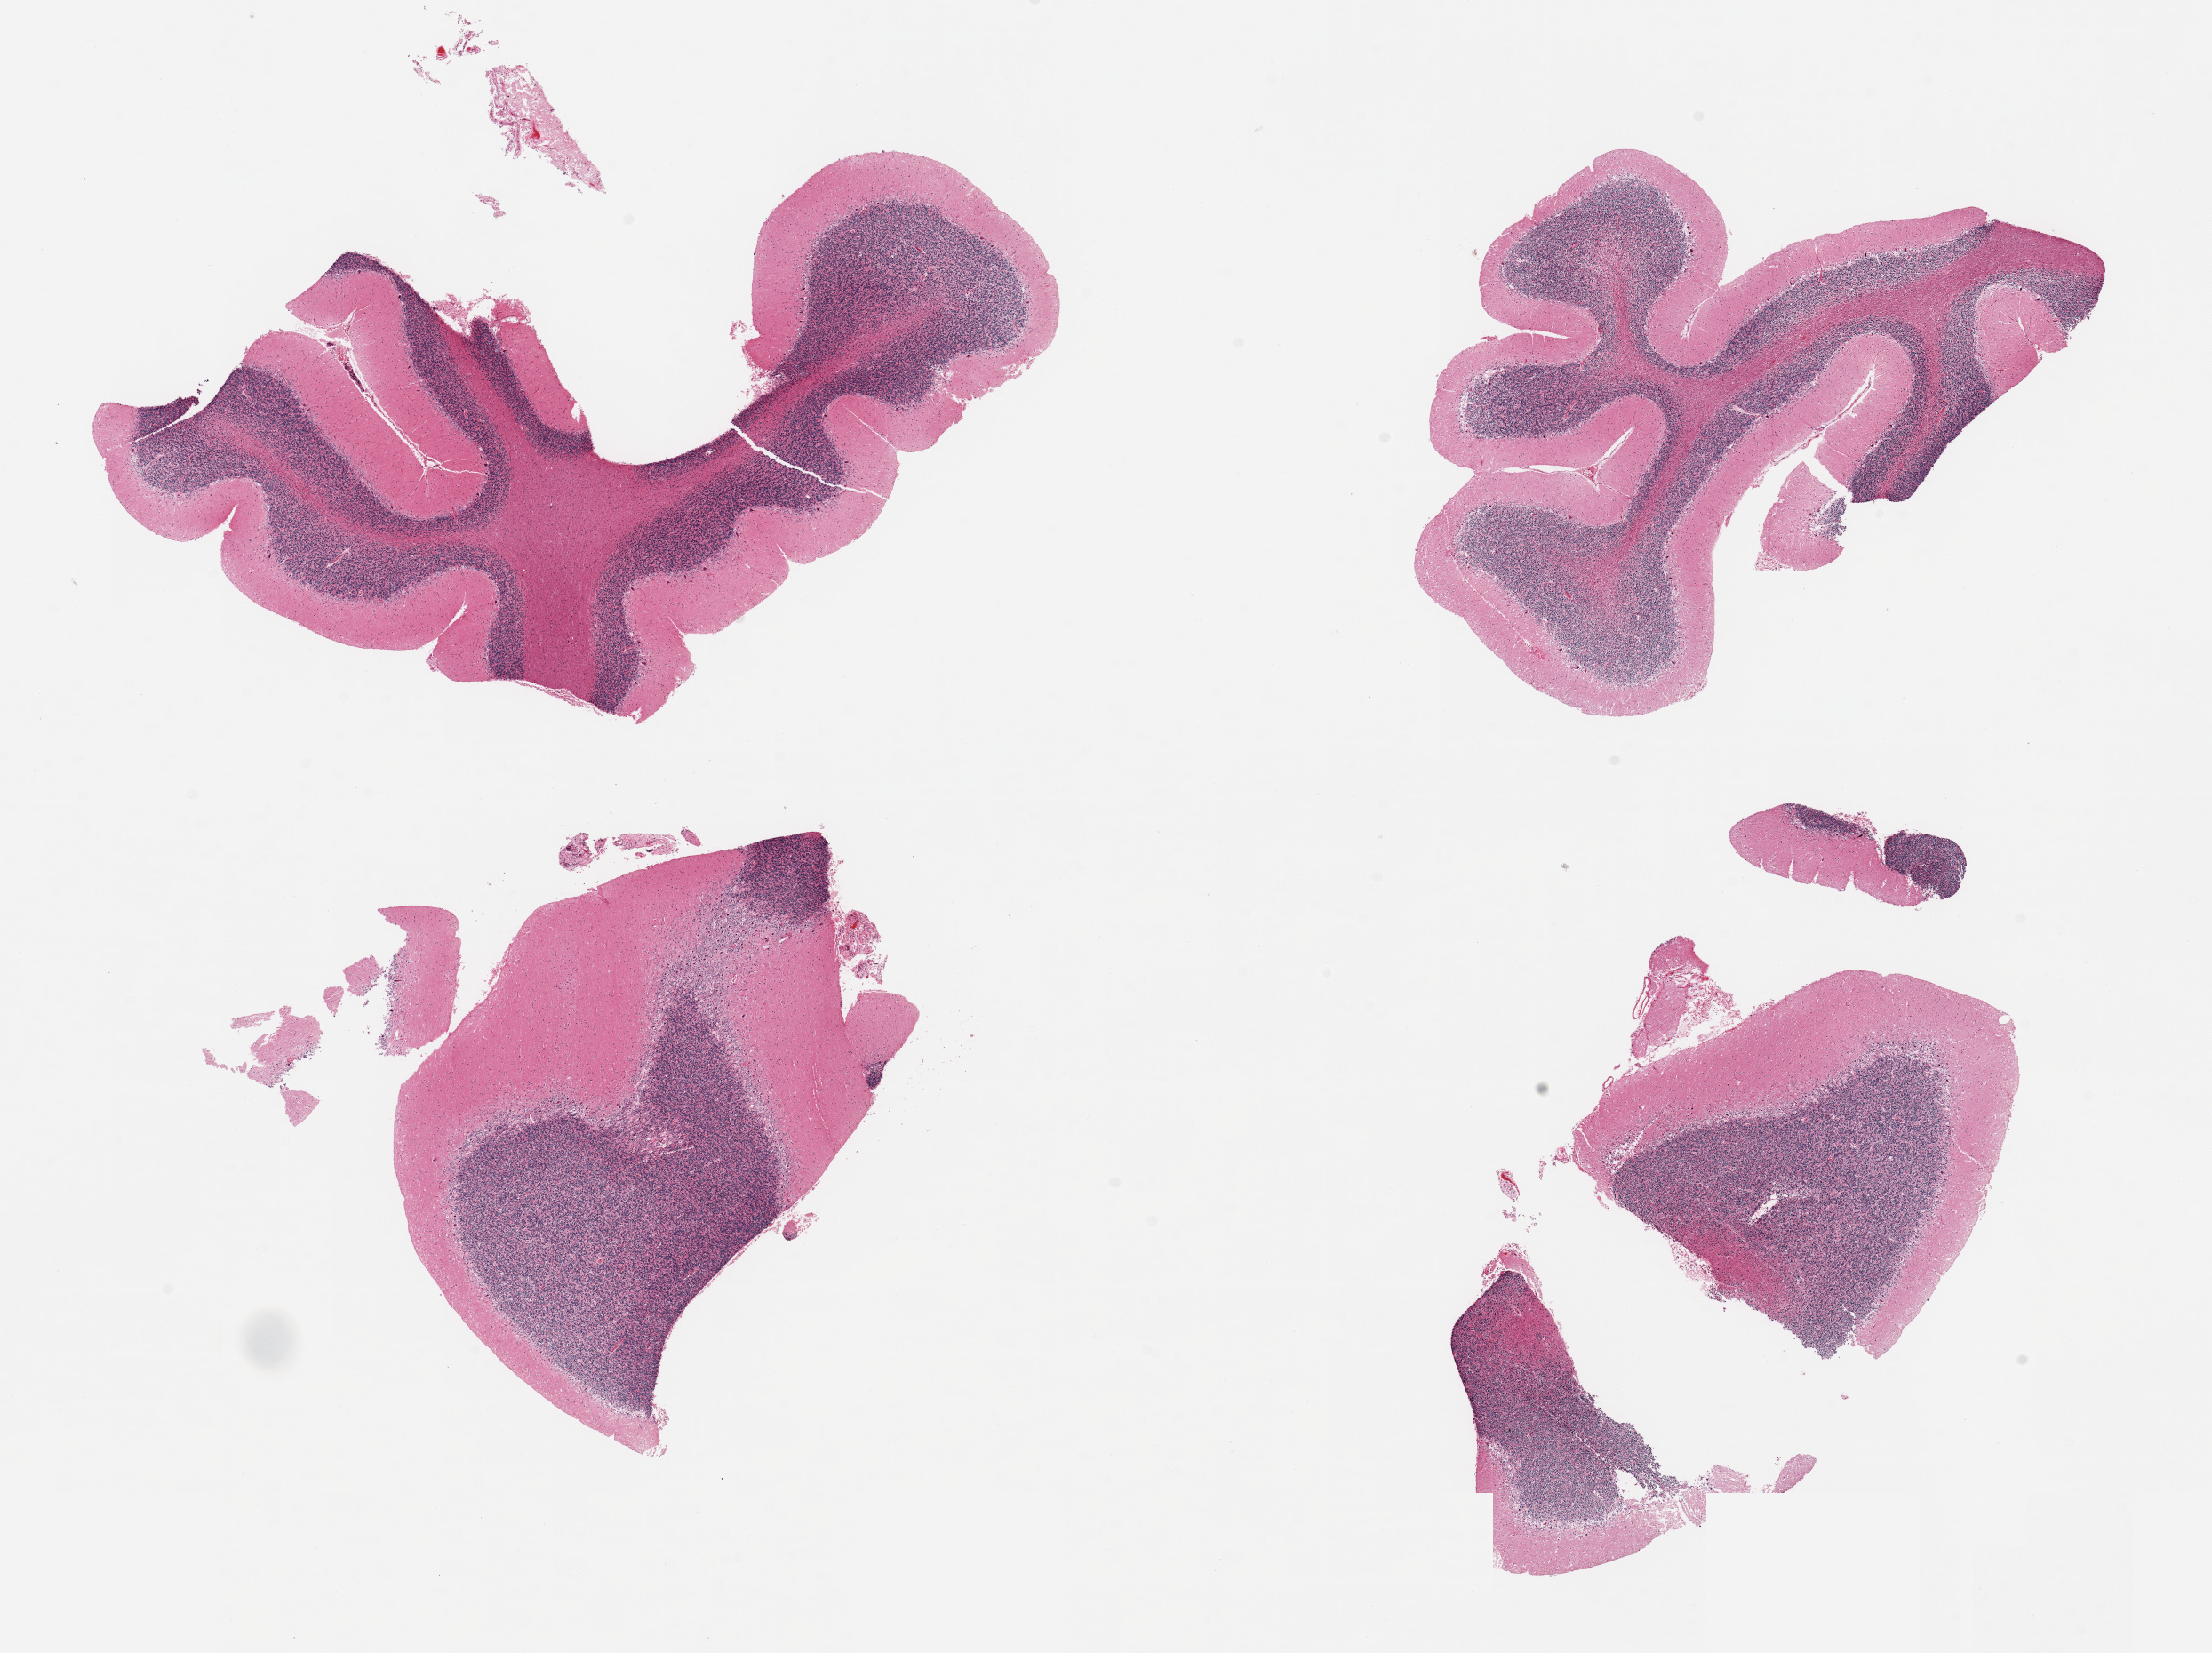
Digitized haematoxylin and eosin-stained section — a low-resolution overview of the entire scanned area, about 19.7 x 14.7 mm (acquisition: 20x scan). PAXgene-fixed paraffin-embedded (PFPE) section. Sampled site (target tissue): cerebellum. Tissue donor sample. Donor sex: male.
Reviewer comment on this tissue sample: 4 pieces, no abnormalities.